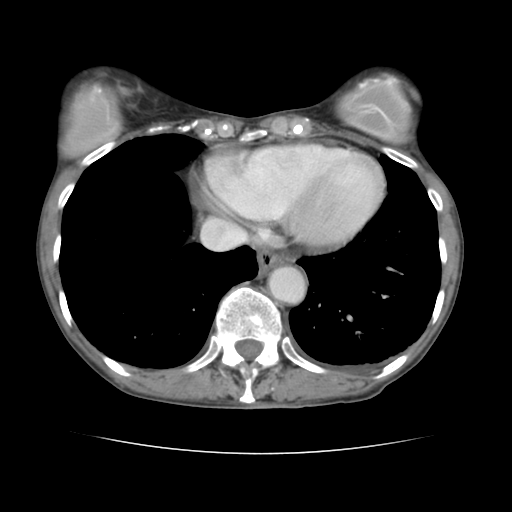
Contrast-enhanced abdominal CT, one axial slice; position 134 of 136 along the scan axis; intravenous contrast given; soft-tissue window (W 400 / L 40 HU); 512 × 512 image matrix, field of view 319 × 319 mm. Female patient, age 77 years. From the clinical record (not read from this slice): diagnosis: colorectal cancer liver metastases, imaged before liver resection; multiple liver metastases: yes; largest metastasis: 3 cm.
Annotated regions visible in this slice (manually delineated by an expert):
- hepatic veins: bounding box (x1, y1, x2, y2) in pixels: (204, 224, 246, 249)